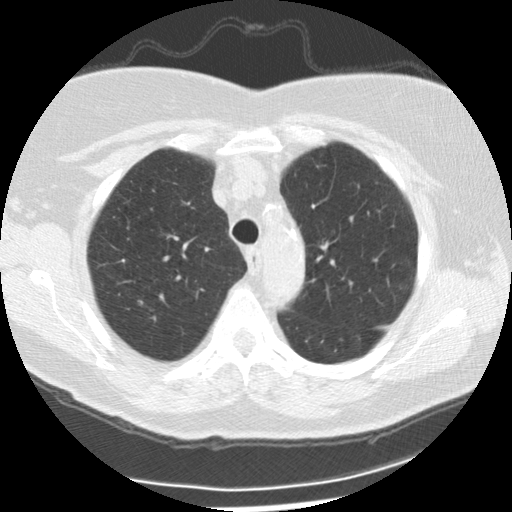
Low-dose screening chest CT, axial slice. Baseline screening round. Lung window (W 1500 / L -600 HU). 2.5 mm slice thickness. Slice 52 of 225 in the series. 512 × 512 image matrix. Female, age 72 years at enrolment. Current smoker at enrolment.
Expert-annotated lung lesion, bounding box (x1, y1, x2, y2) in pixels: (124, 292, 152, 317). No non-calcified nodule or mass ≥4 mm was recorded by the screening reader at this exam. Official screen result: negative screen, minor abnormalities not suspicious for lung cancer. Later outcome: lung cancer diagnosed 877 days after this screen (after the third annual screen) — squamous cell carcinoma, NOS, right upper lobe, poorly differentiated (G3), stage IIIA (AJCC 6th edition), 22 mm at pathology.